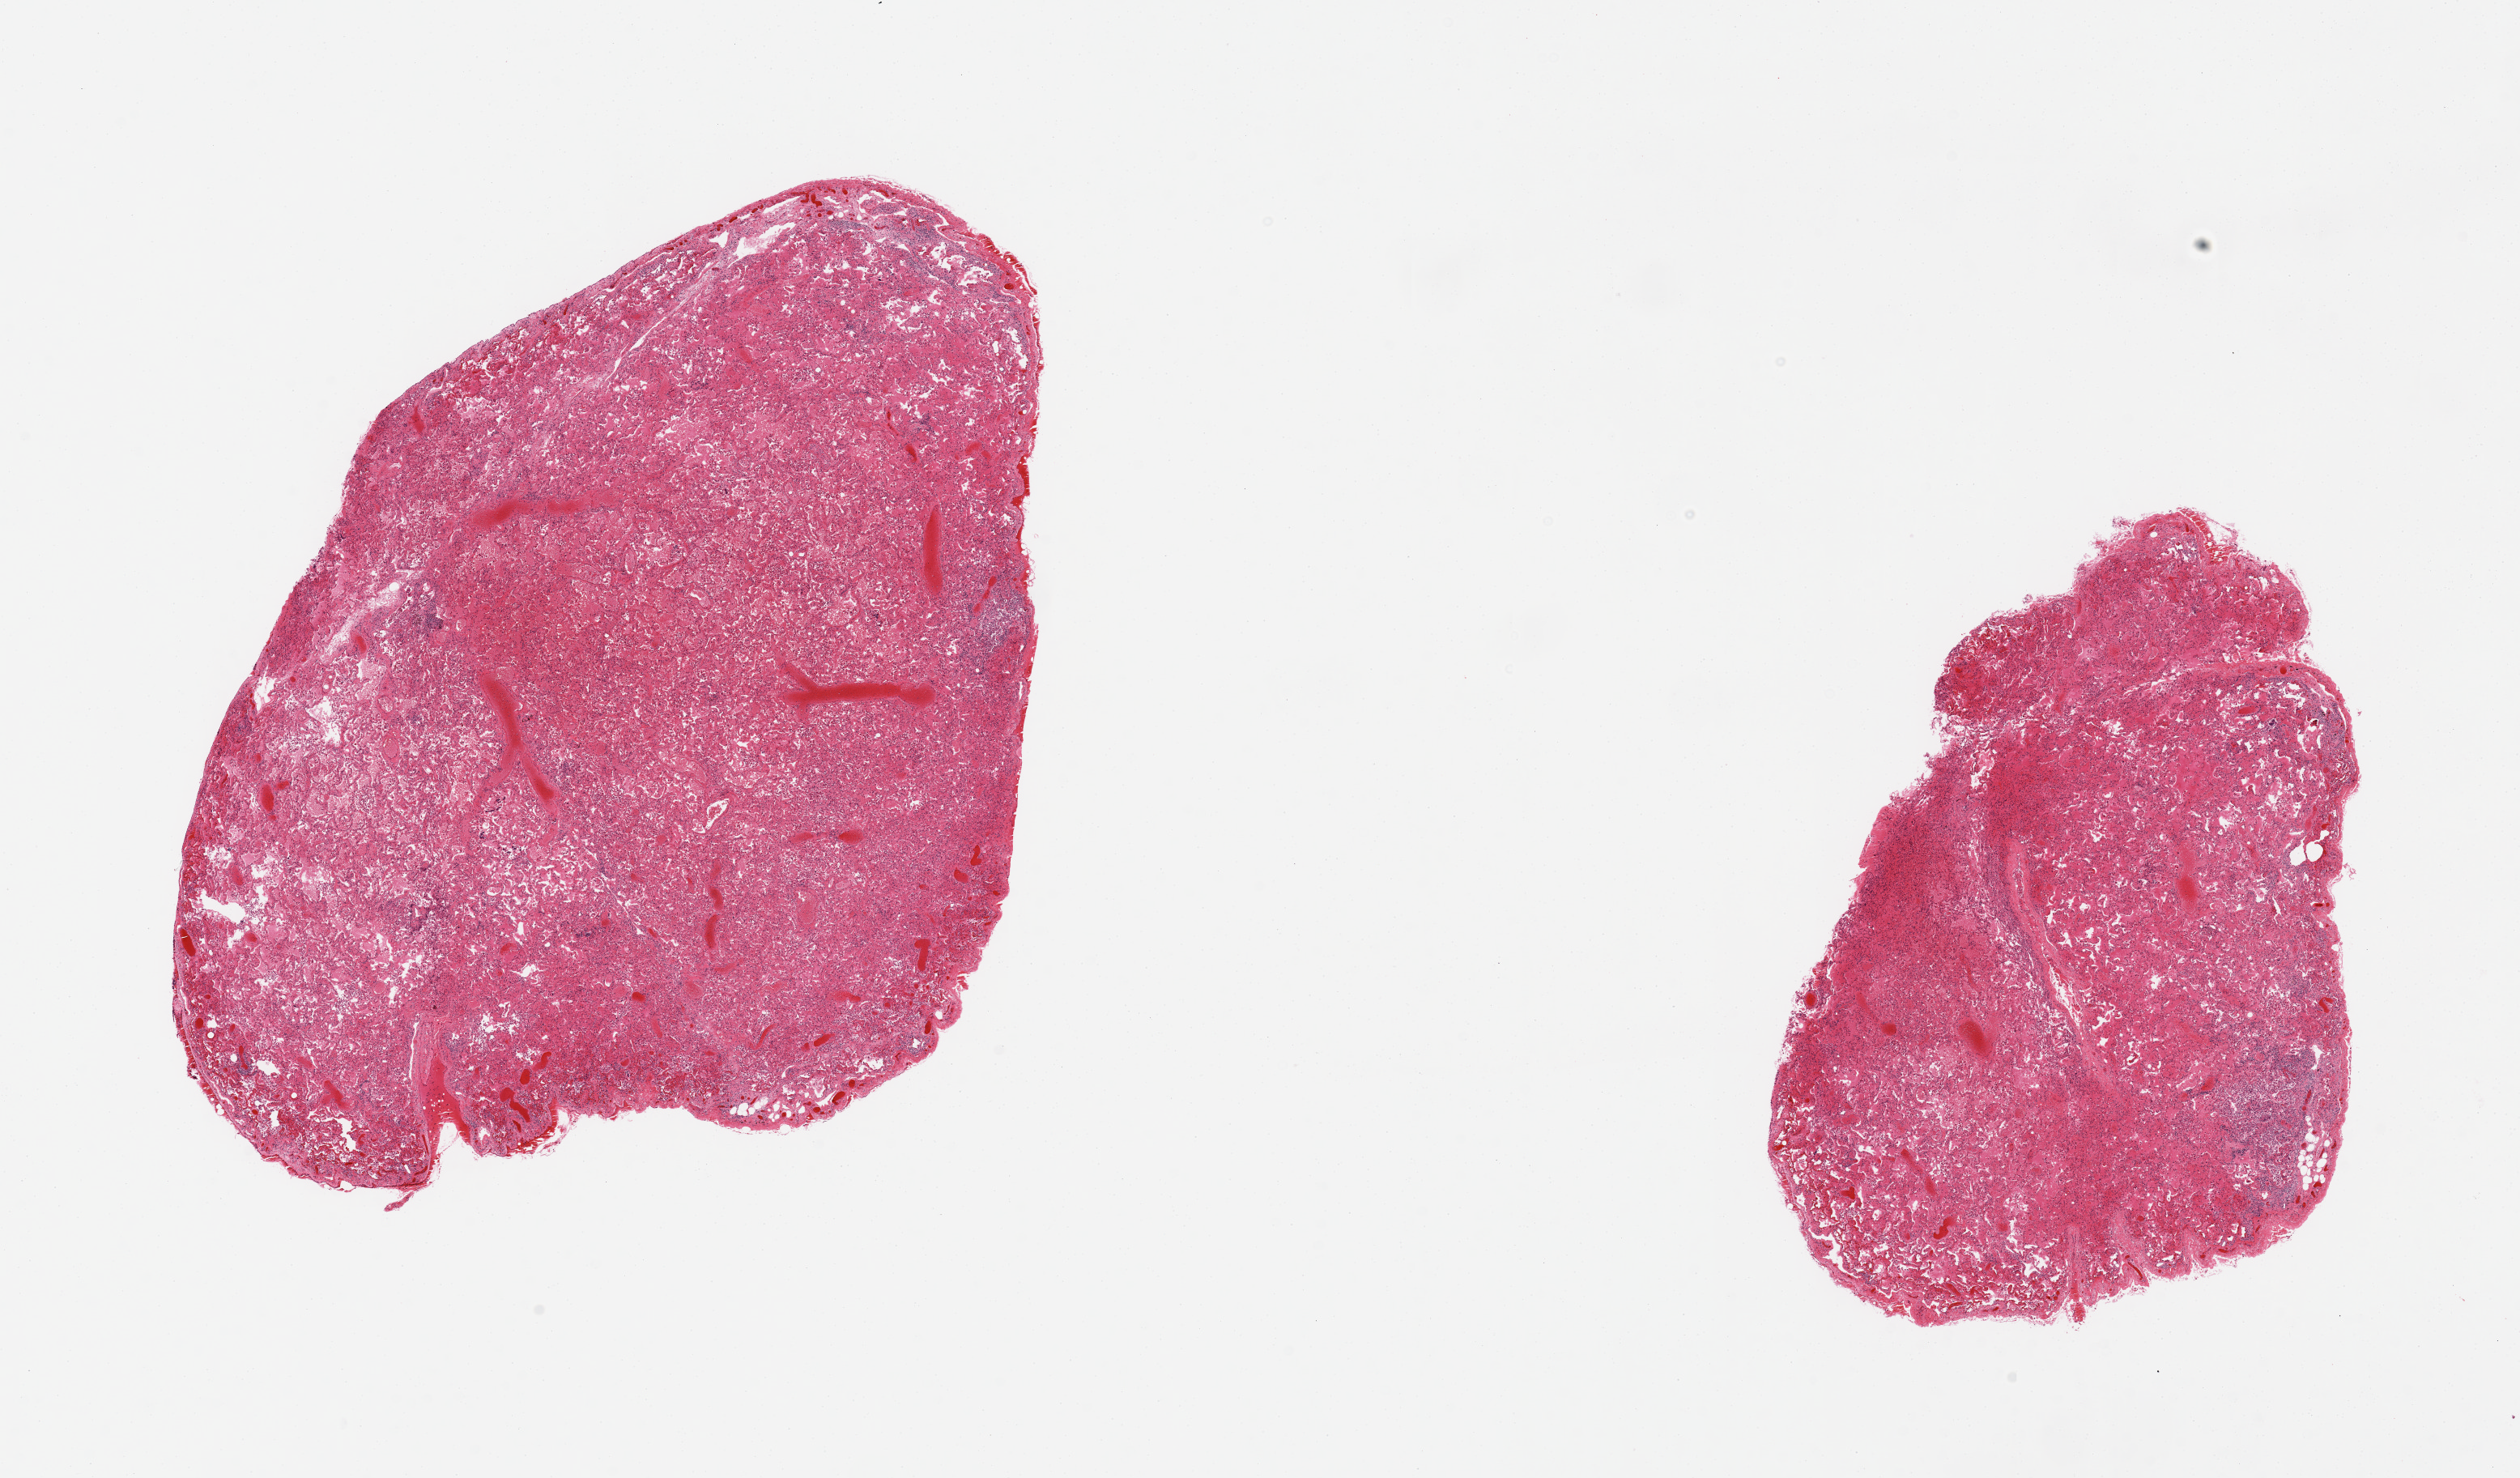
Digitized haematoxylin and eosin-stained section, brightfield, whole scanned area (about 24.6 x 14.4 mm) shown as a low-resolution overview, PAXgene-fixed paraffin-embedded (PFPE) section, target tissue: lung, donor tissue sample. Donor: male.
Review note (as recorded): 2 pieces, severe congestion and edema, numerous hemosiderin-laden macrophages.